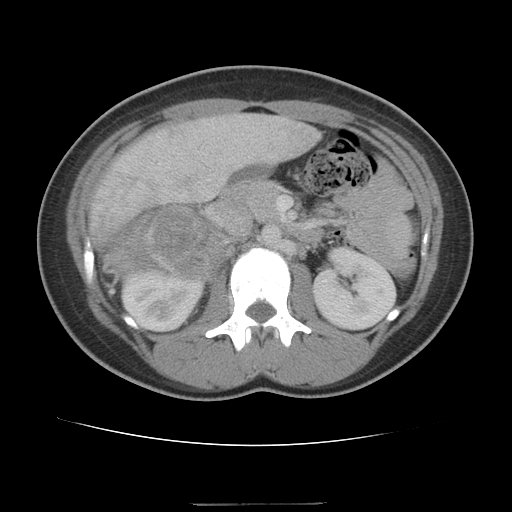
Contrast-enhanced abdominal CT, one axial slice. Slice 62 of 100 in the series (ordered by position). Reconstruction kernel STANDARD. Intravenous contrast given. Soft-tissue window (W 400 / L 40 HU). 512 × 512 image matrix, field of view 360 × 360 mm. Patient: female, 21 years. From the clinical record (not read from this slice): diagnosis: adrenocortical carcinoma; tumour side: right adrenal; tumour size at pathology: 15.5 cm; Ki-67 index: 26 %; stage (as recorded): 3.
Outlined on this slice (semi-automatic segmentation, software-assisted and operator-edited):
- mass: bounding box (x1, y1, x2, y2) in pixels: (112, 208, 222, 277)